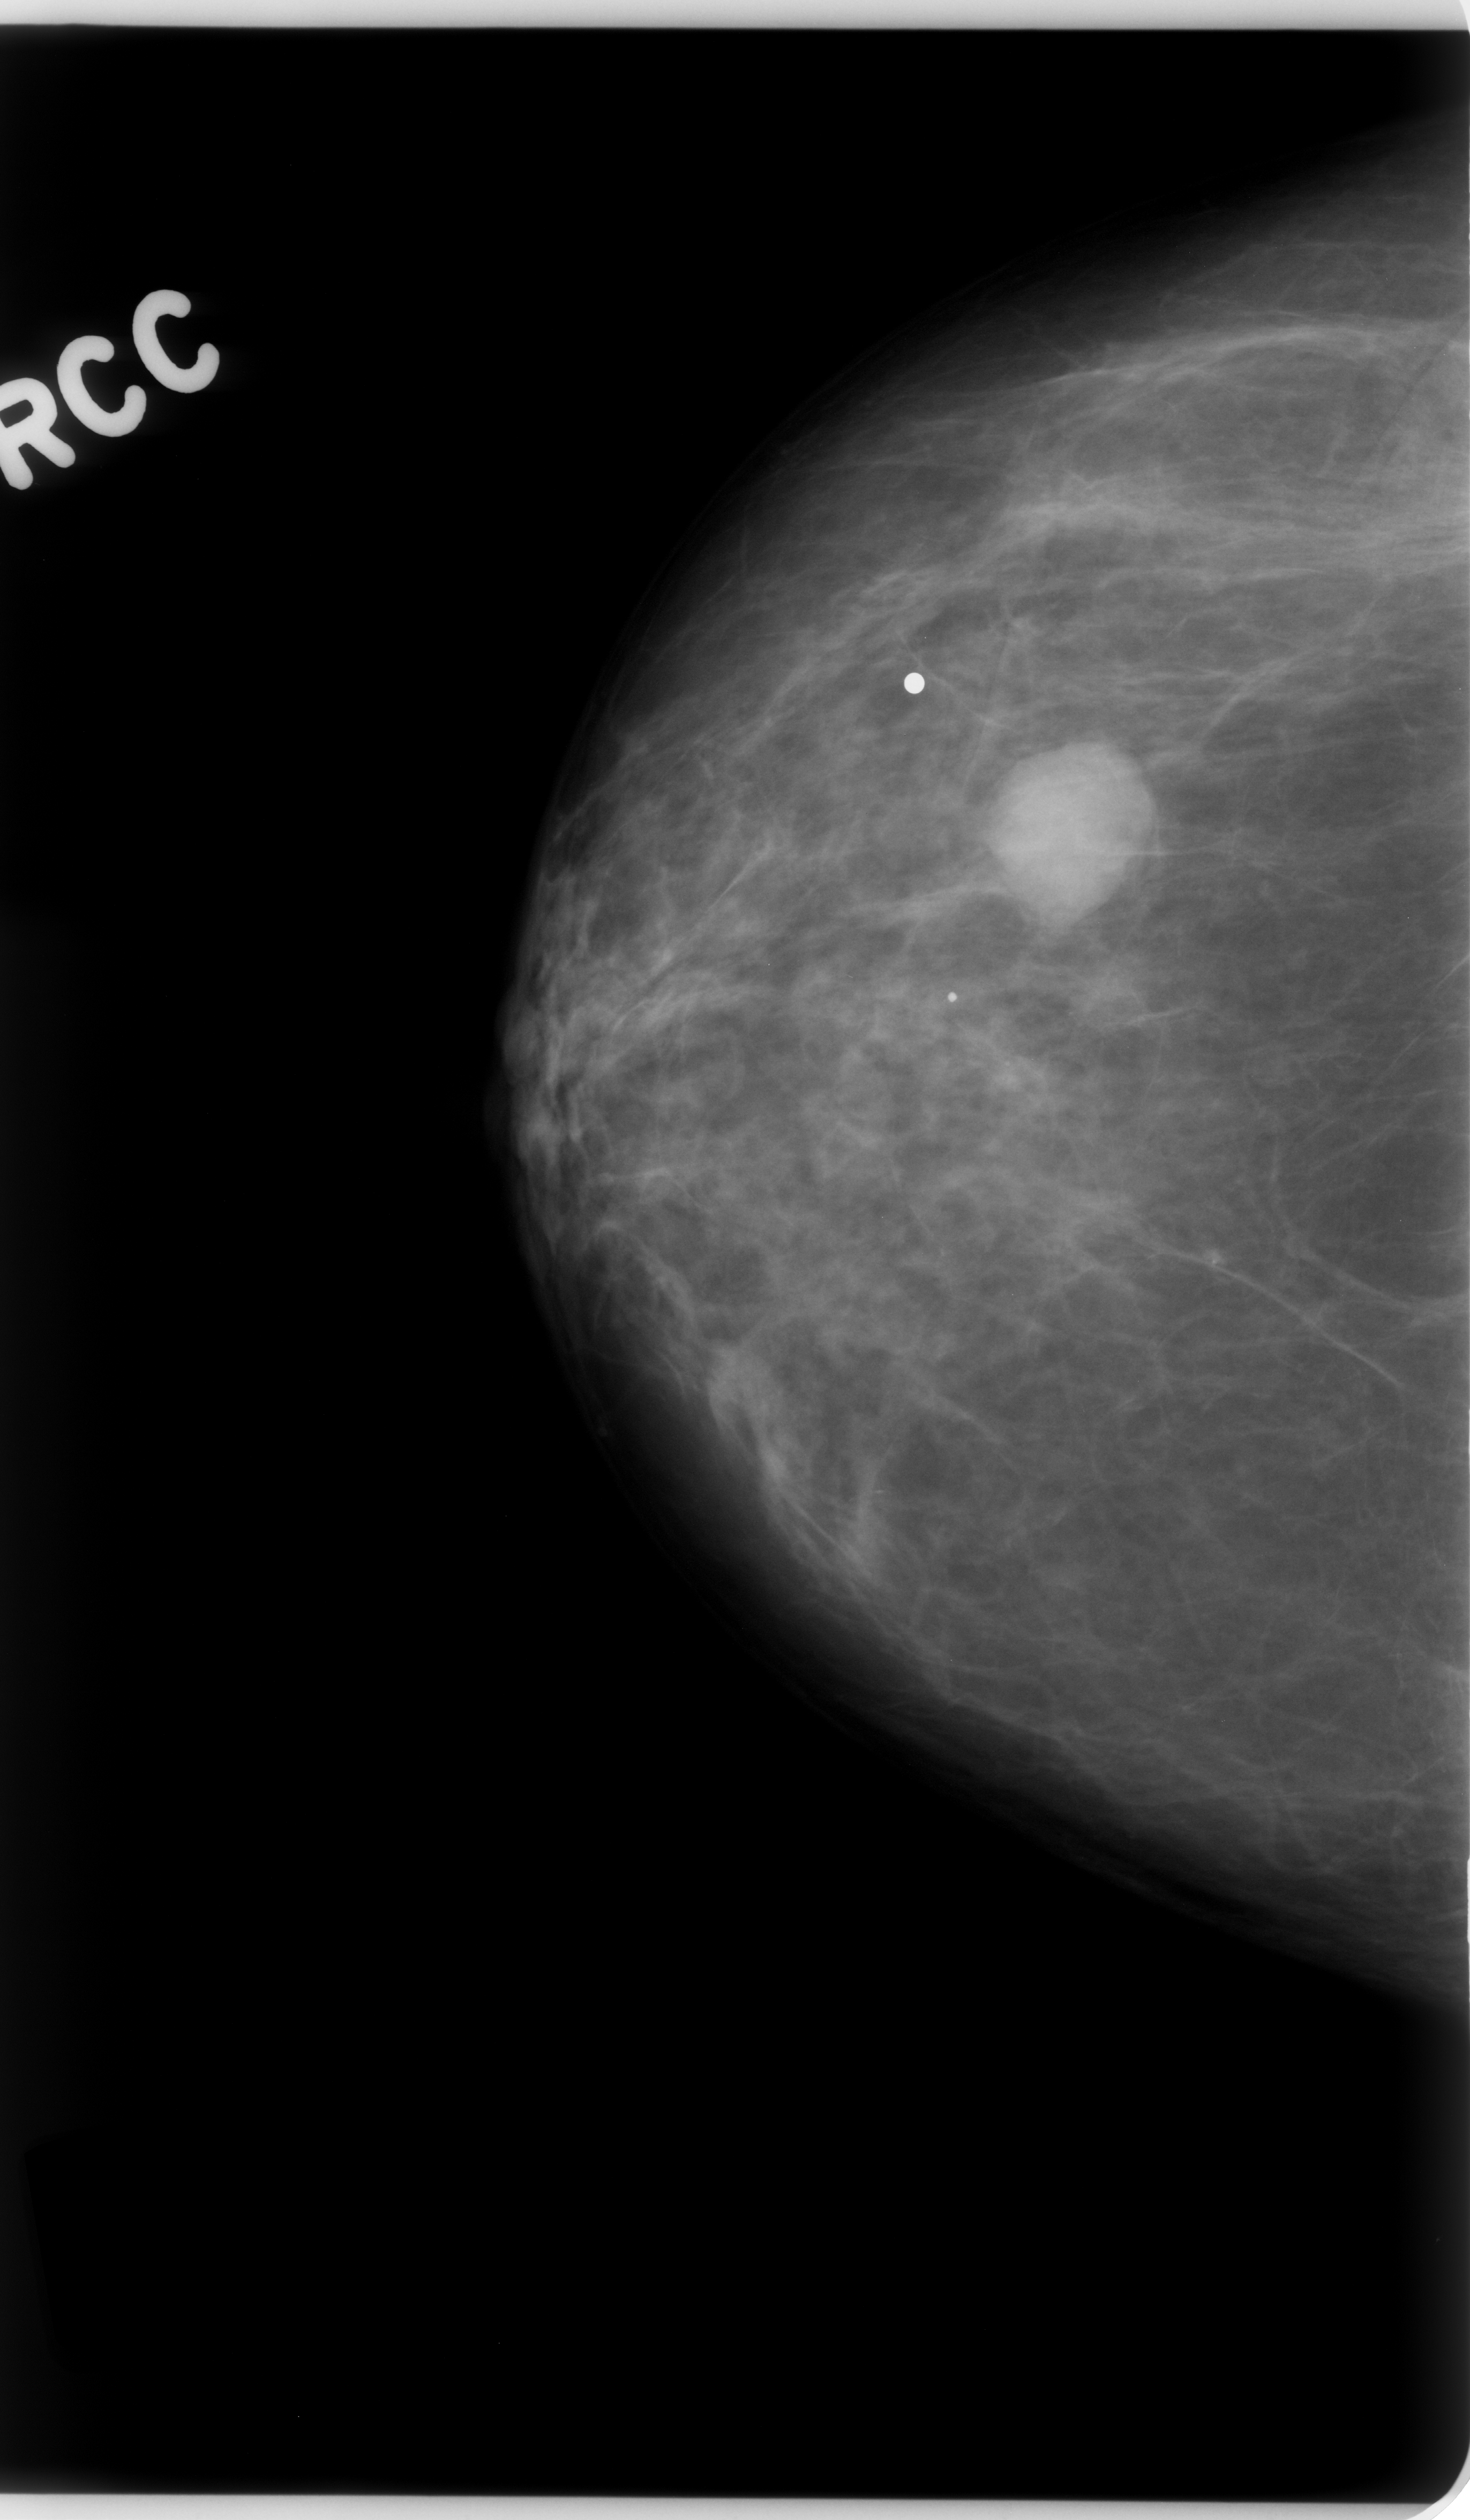
Scanned film-screen mammogram. Right breast. Craniocaudal (CC) view. Breast composition: scattered fibroglandular densities (BI-RADS density category 2 of 4). 1470 × 2520 image matrix.
Expert-marked regions of interest on this film, with their recorded descriptors:
- mass, shape round, margins circumscribed; BI-RADS assessment category 4; subtlety rating 5 on a 1 (subtle) to 5 (obvious) scale; pathology result (as recorded, not read from the image): benign: box from (x=987, y=736) to (x=1174, y=928) px